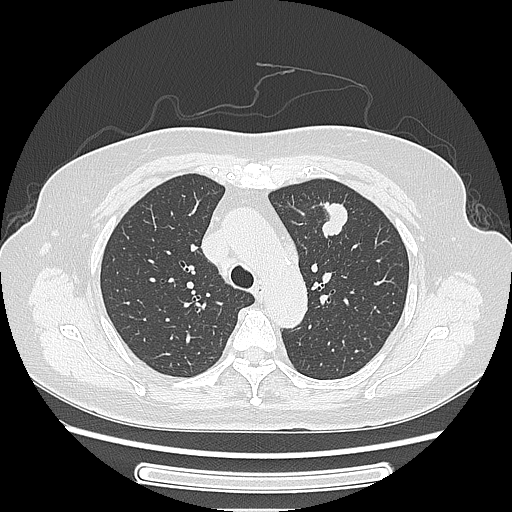
Chest CT, one axial slice; position 173 of 227 along the scan axis; reconstruction kernel LUNG; lung window (W 1500 / L -600 HU); 1.25 mm slice thickness; 512 × 512 image matrix, field of view 363 × 363 mm. Patient: female, 77 years. From the clinical record (not read from this slice): clinical TNM (as recorded): T1c N3 M0; histopathological grade: G2-3.
Annotated regions visible in this slice (rectangle marked by the reading radiologist):
- lung tumour (recorded histology: adenocarcinoma): bounding box [x1, y1, x2, y2] px = [308, 193, 358, 247]